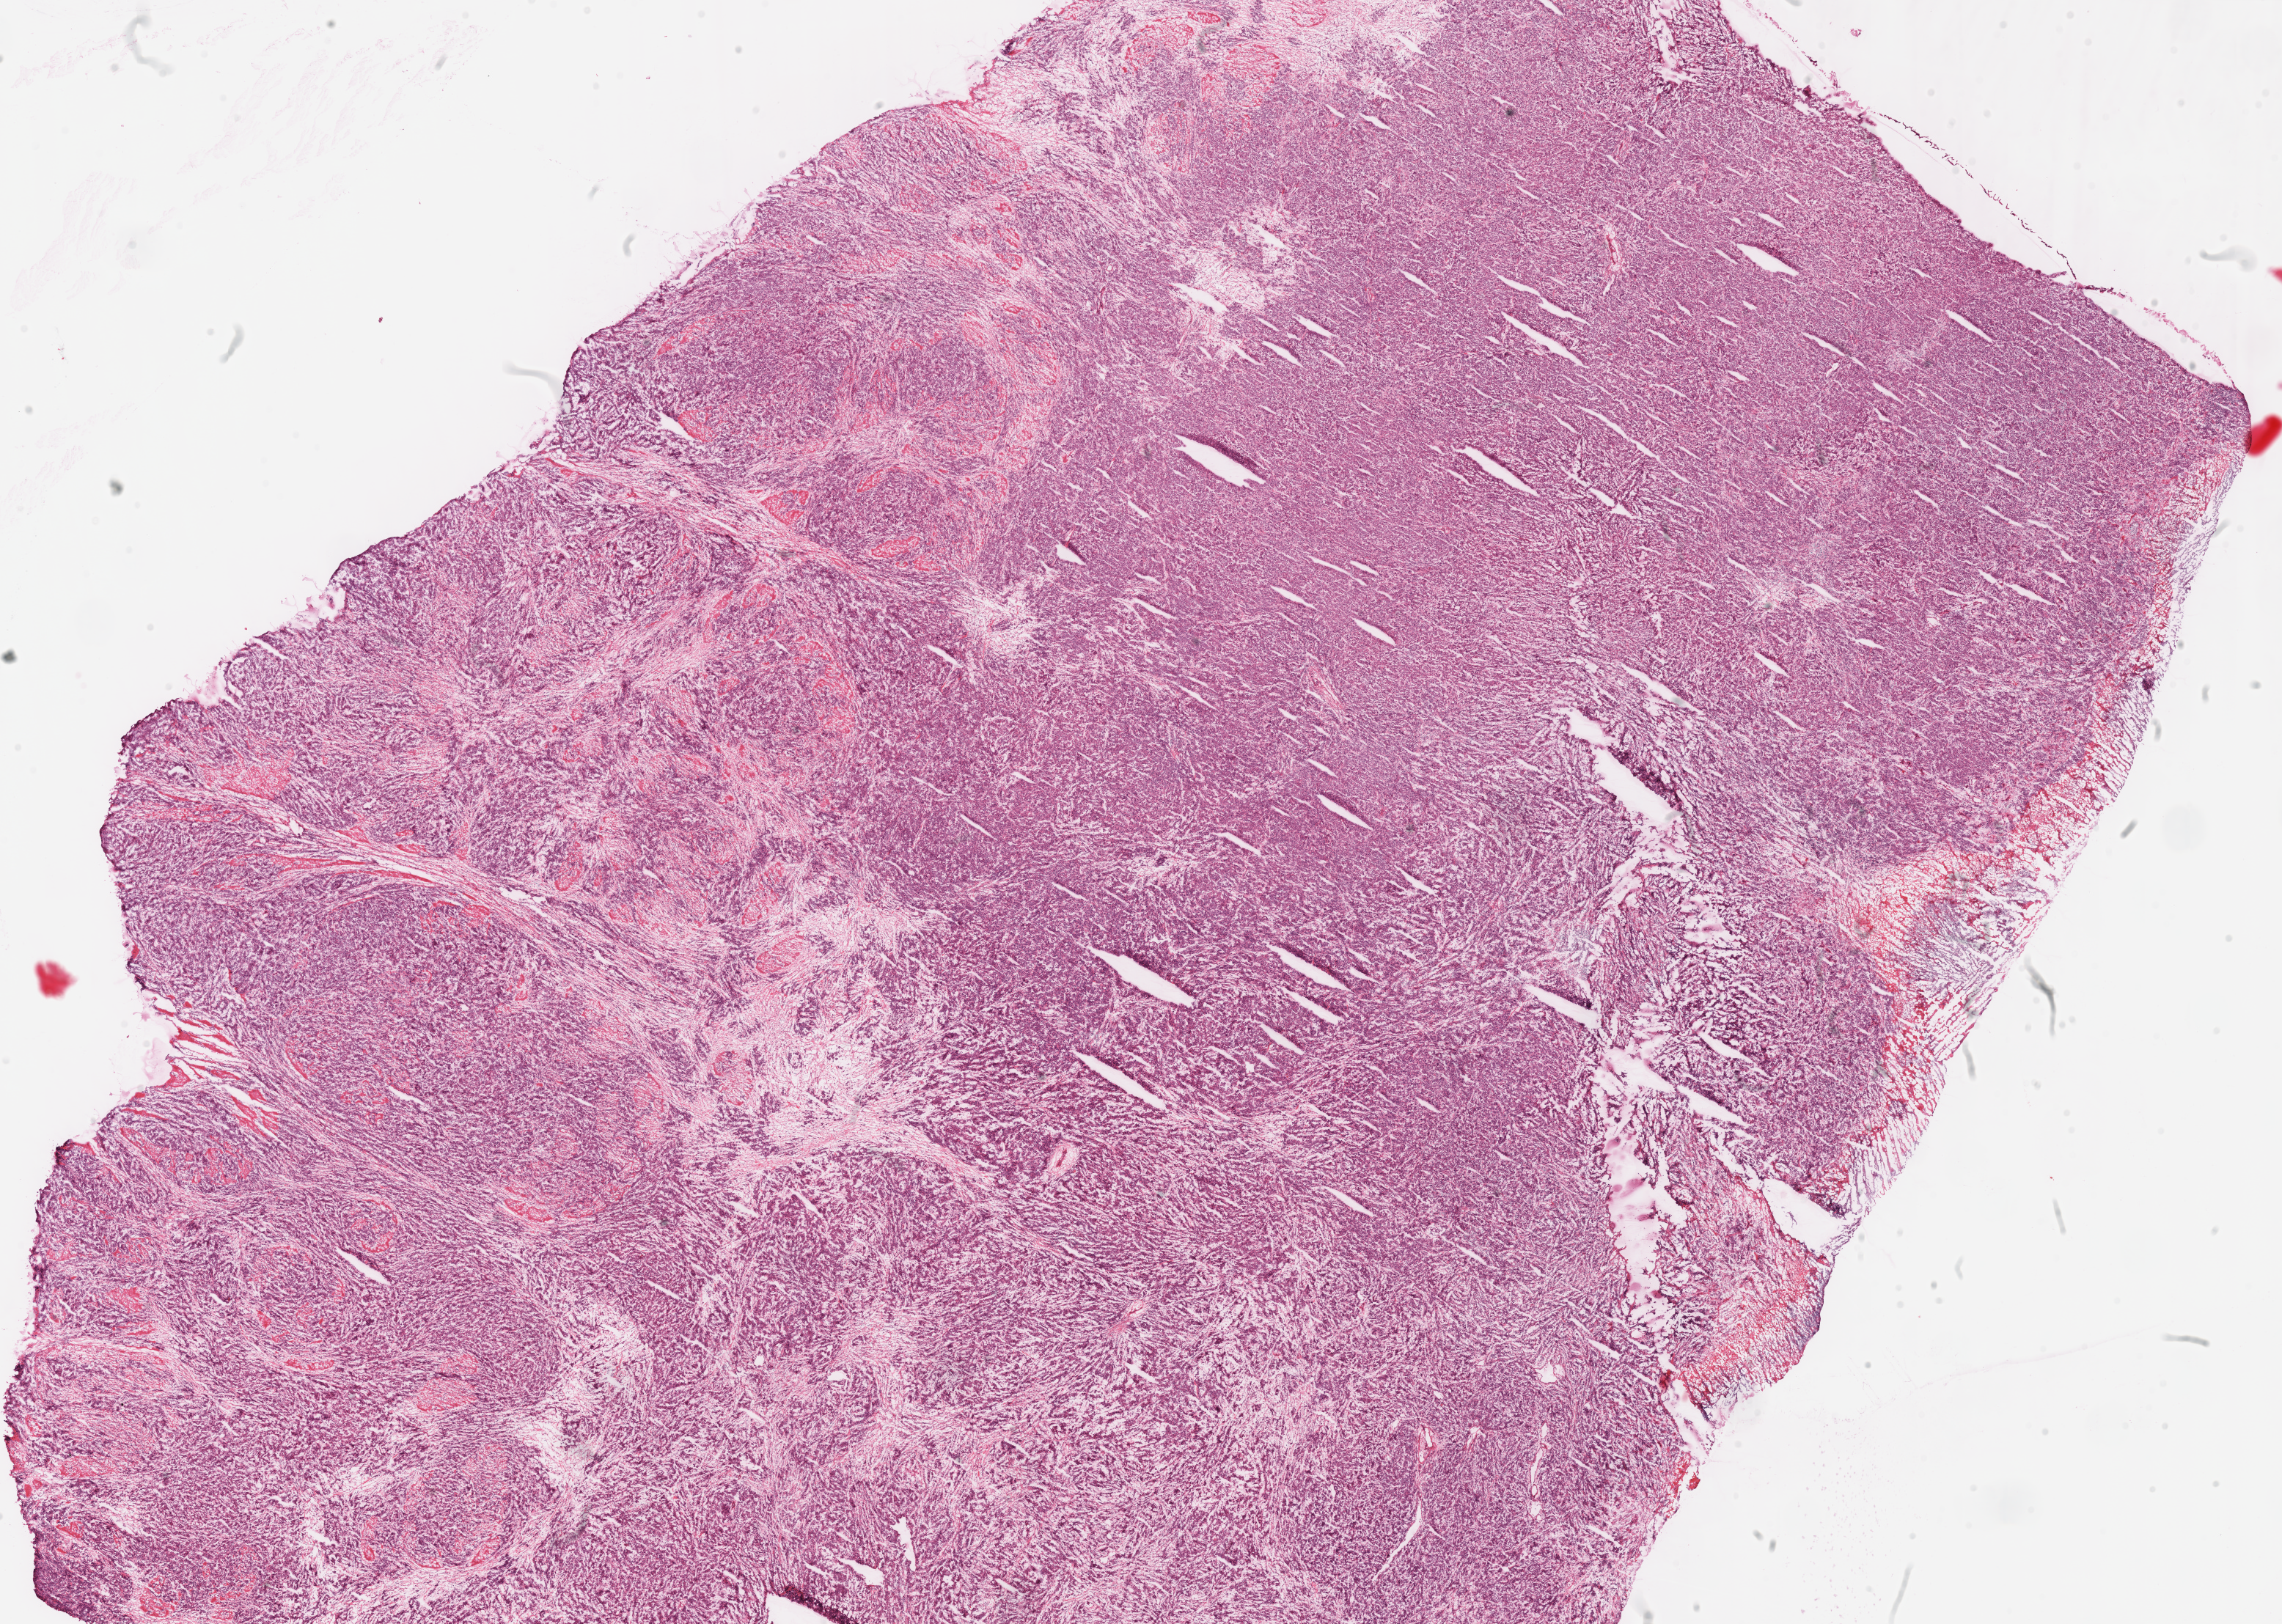
H&E-stained whole-slide image — whole scanned area (about 24.5 x 17.4 mm, acquisition: 40x scan) shown as a low-resolution overview. Frozen section from the top of the tissue portion. Stomach, primary tumour sample. Female patient; age at initial diagnosis 71 years. Histologic grade: G3 (poorly differentiated). Pathologist review of this section (percent, as recorded): tumour cells 85%, tumour nuclei 75%, normal cells 0%, stromal cells 10%, necrosis 5%.
• AJCC pathologic stage: IIIC
• histologic diagnosis: Adenocarcinoma, NOS (fundus of stomach)
• lymph nodes positive (case pathology): 6 of 10 examined